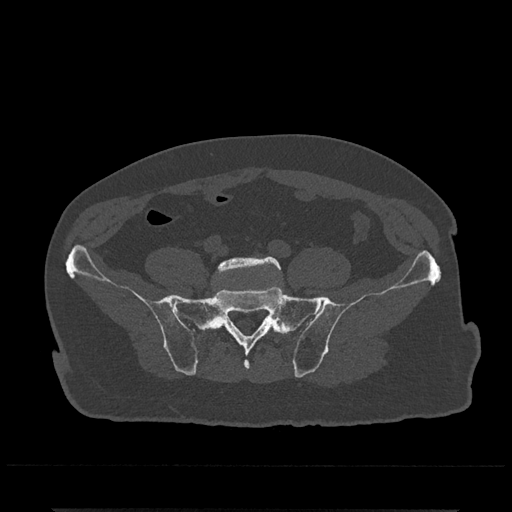
CT including the spine, one axial slice. Slice 39 of 797 in the series (ordered by position). 120 kVp. Bone window (W 1800 / L 400 HU). 512 × 512 image matrix. Patient: male, 67 years. Case-level facts recorded for this patient, not image findings: primary cancer: prostate.
Structures marked on this image (semi-automatic segmentation, software-assisted and operator-edited):
- L5 vertebra: bounding box <213,256,282,288> (left, top, right, bottom; pixels)